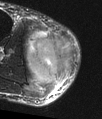
MRI of an extremity soft-tissue mass, one axial slice; position 31 of 48 along the scan axis; T2-weighted fat-saturated; MR volume resampled by the dataset authors to the PET/CT grid (not the native acquisition matrix); 102 × 119 image matrix, field of view 100 × 116 mm. Male patient. Case-level facts recorded for this patient, not image findings: histological type: pleiomorphic liposarcoma; grade: high; site of the primary tumour: right calf.
Structures marked on this image (expert contour drawn on MRI and transferred to this co-registered scan by the dataset authors):
- gross tumour volume including surrounding oedema: bounding box (x1, y1, x2, y2) in pixels: (25, 28, 75, 88)
- gross tumour volume (mass): (28, 35, 75, 84)